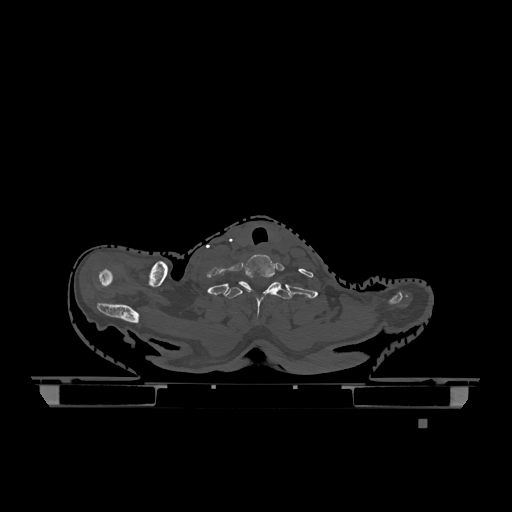
CT including the spine, one axial slice. Position 1012 of 1317 along the scan axis. Bone window (W 1800 / L 400 HU). 0.5 mm slice thickness. 512 × 512 image matrix, field of view 500 × 500 mm. Female patient, age 74 years. From the clinical record (not read from this slice): primary cancer: lung; vertebrae with lytic lesions (as recorded): T1, T4, T5, T6, L4, L5.
Annotated regions visible in this slice (semi-automatically segmented with operator editing):
- T1 vertebra: bounding box (x1, y1, x2, y2) in pixels: (223, 281, 291, 317)